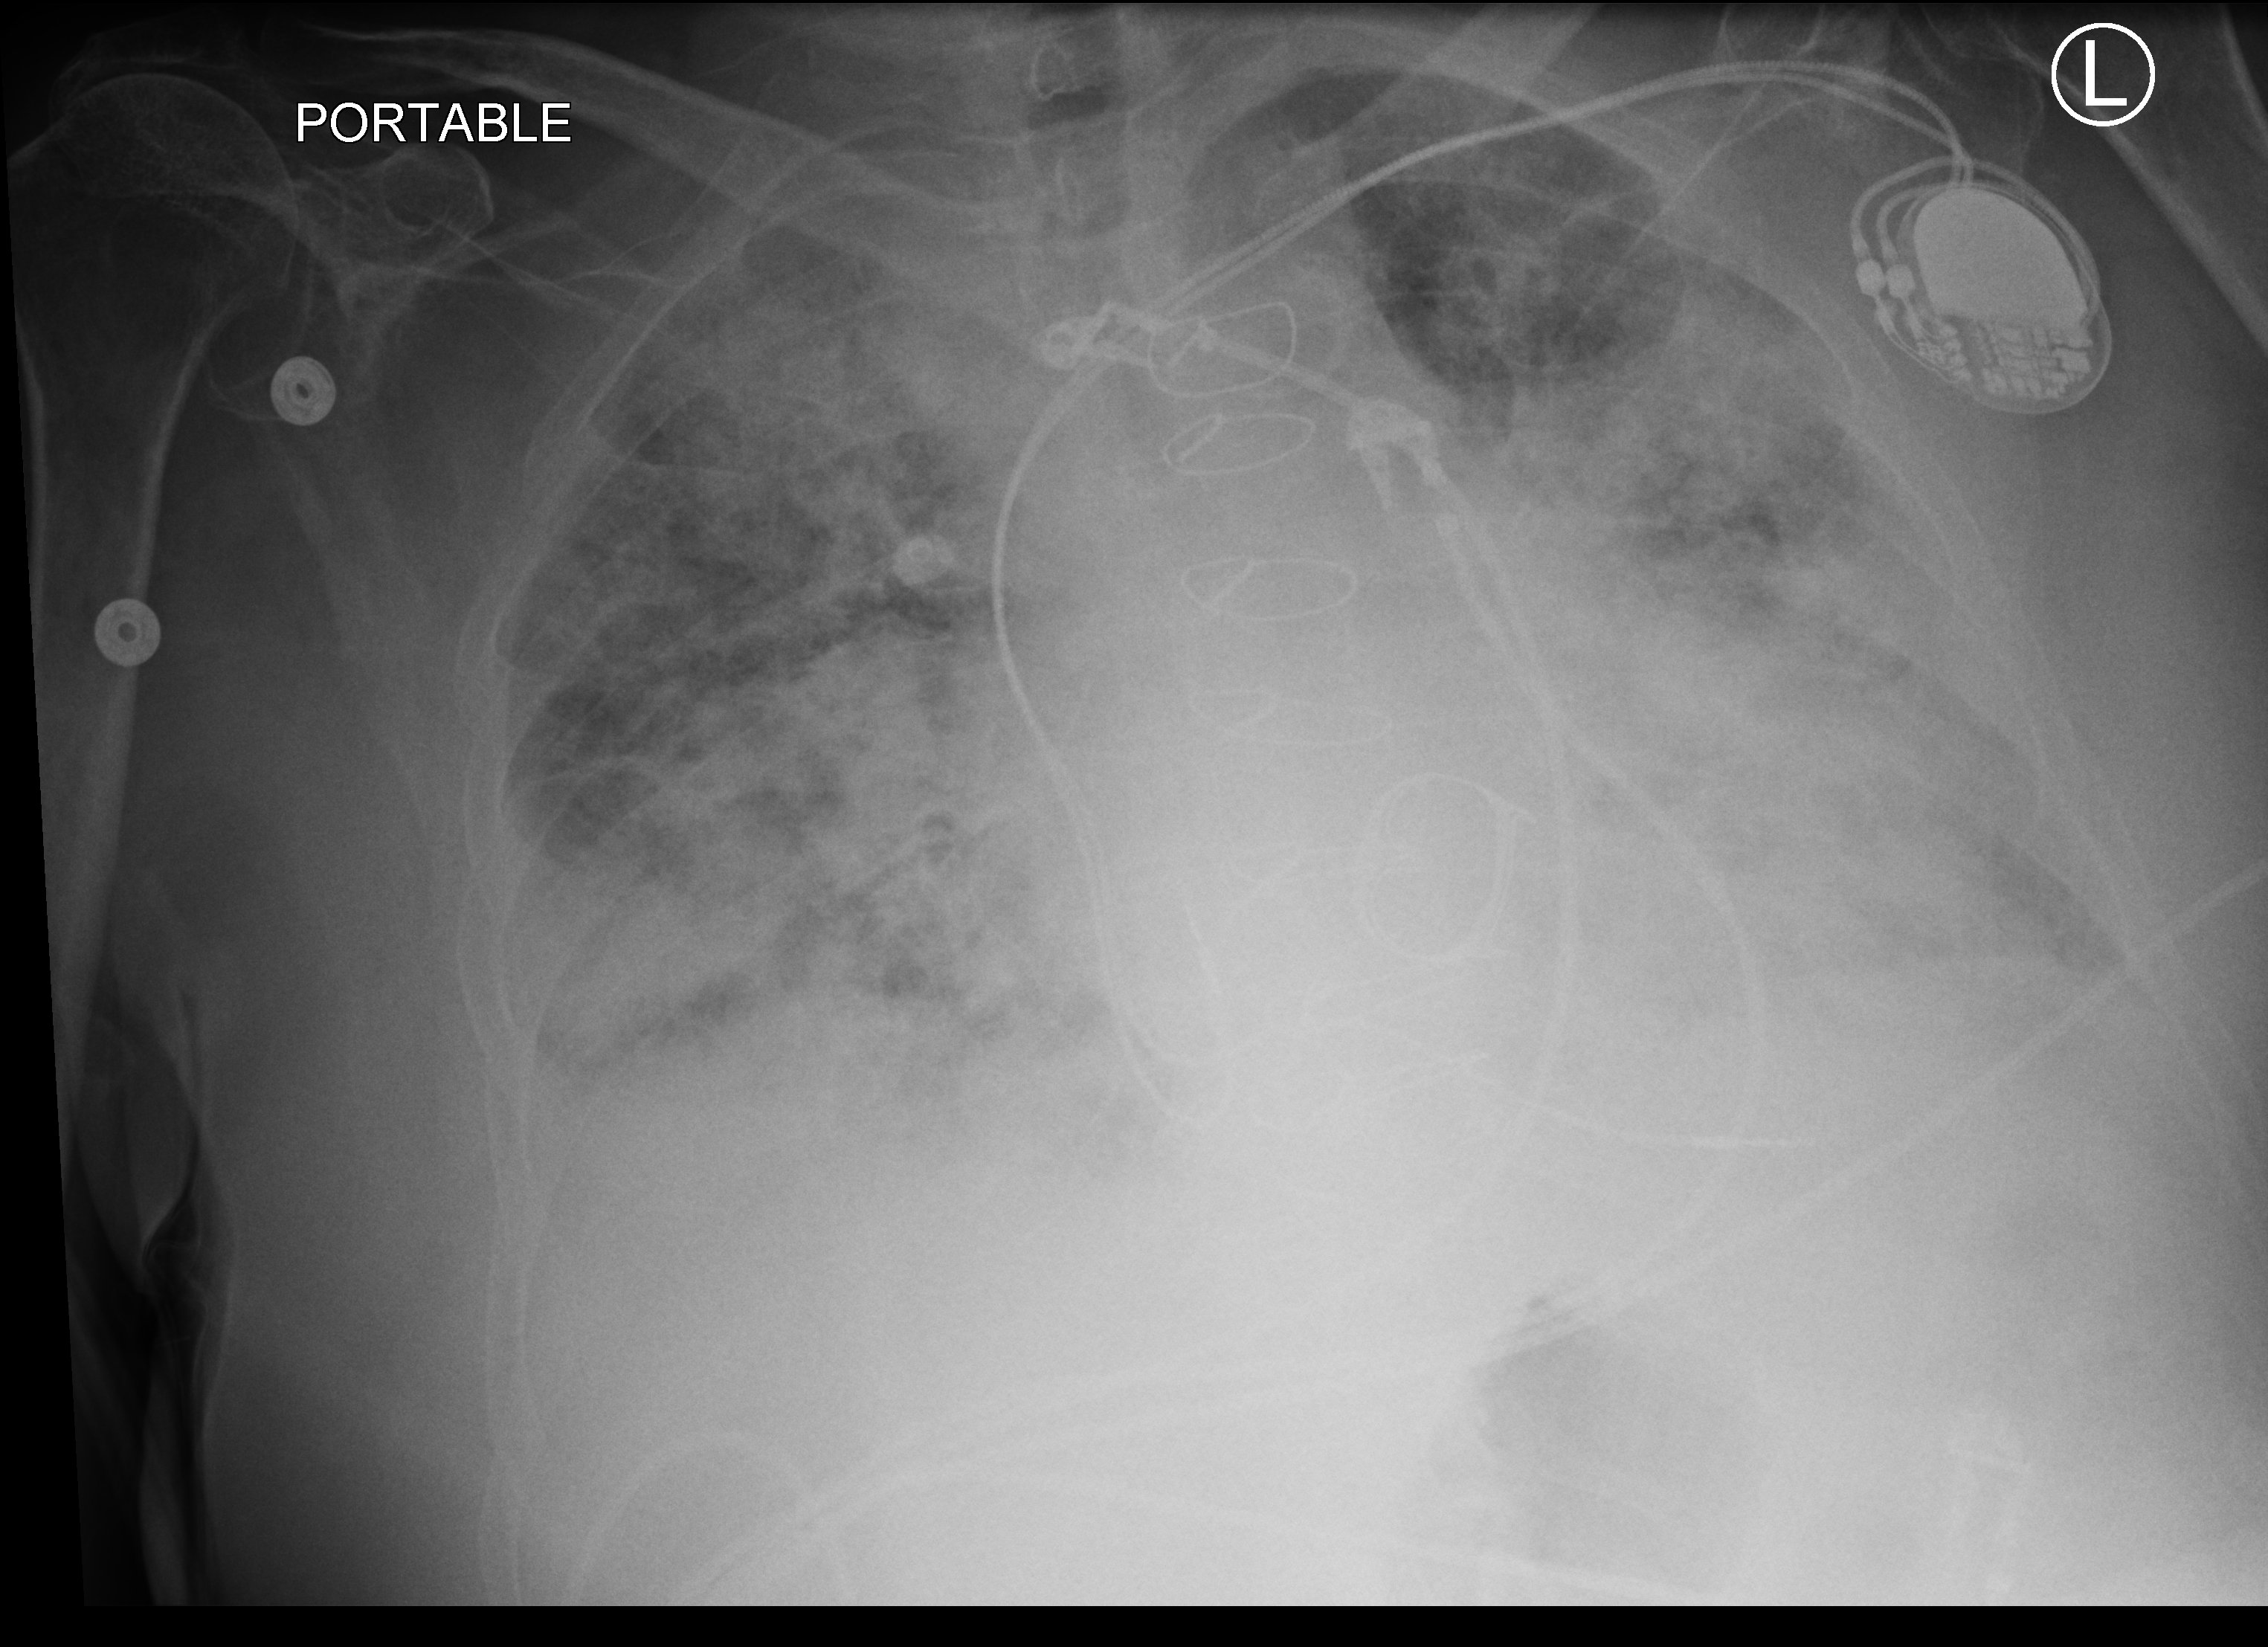
Bedside chest radiograph (computed radiography). Patient hospitalised with COVID-19; male, aged 75–90 years.
Admission-level facts for this patient (not findings on this image; timing relative to this image not recorded): mechanically ventilated during this hospital stay: no; length of hospital stay: 13 days.